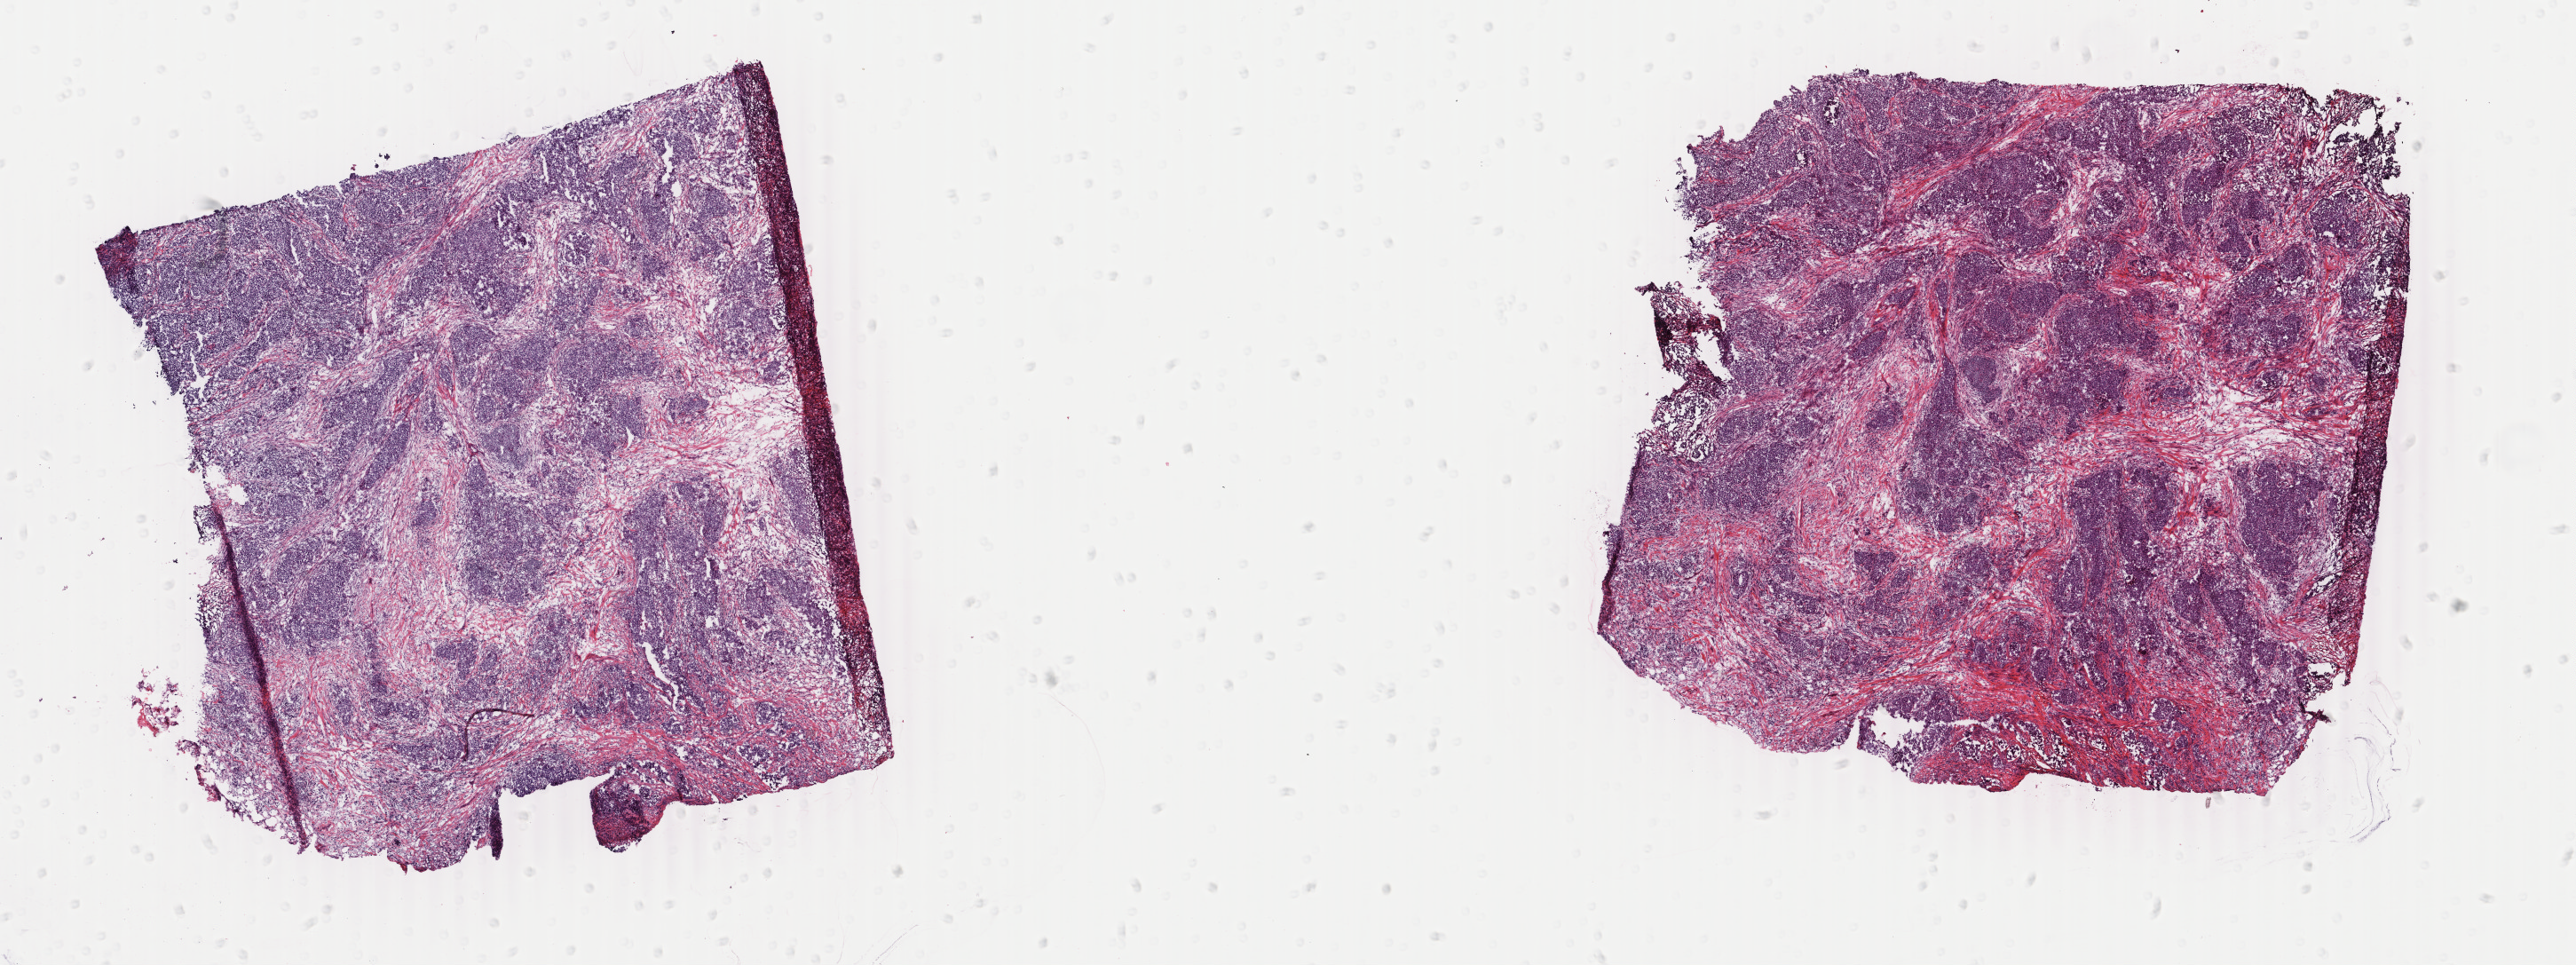
Digitized H&E-stained tissue section (whole slide), a low-resolution overview of the entire scanned area, about 23.1 x 8.6 mm, frozen section from the top of the tissue portion, primary tumour sample from the breast. Patient: female, age at initial diagnosis 64 years. Pathologist review of this section (percent, as recorded): tumour cells 75%, tumour nuclei 75%, normal cells 0%, stromal cells 25%, necrosis 0%. Infiltration values recorded for this section: lymphocyte infiltration 5%, monocyte infiltration 0%, neutrophil infiltration 0%.
Pathologic diagnosis: Infiltrating duct carcinoma, NOS. Lymph nodes positive (case pathology): 0 of 2 examined. AJCC pathologic stage: IIA (6th edition). Laterality: left.